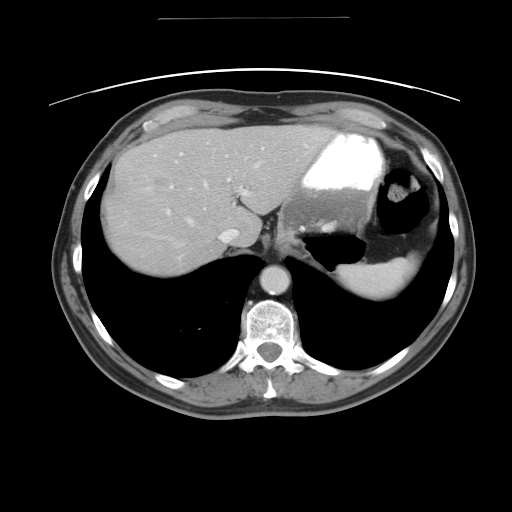
Contrast-enhanced abdominal CT, one axial slice; position 37 of 49 along the scan axis; reconstruction kernel STANDARD; intravenous contrast given; soft-tissue window (W 400 / L 40 HU); 5 mm slice thickness; 512 × 512 image matrix, field of view 413 × 413 mm. Male patient, age 57 years. From the clinical record (not read from this slice): diagnosis: colorectal cancer liver metastases, imaged before liver resection; multiple liver metastases: yes; largest metastasis: 4 cm.
Annotated regions visible in this slice (manually delineated by an expert):
- hepatic veins: bounding box <184,162,257,225> (left, top, right, bottom; pixels)
- liver: <103,125,333,276>
- planned liver remnant (the part of the liver to remain after resection): <207,125,332,246>
- portal vein (with intrahepatic branches): <164,141,263,215>